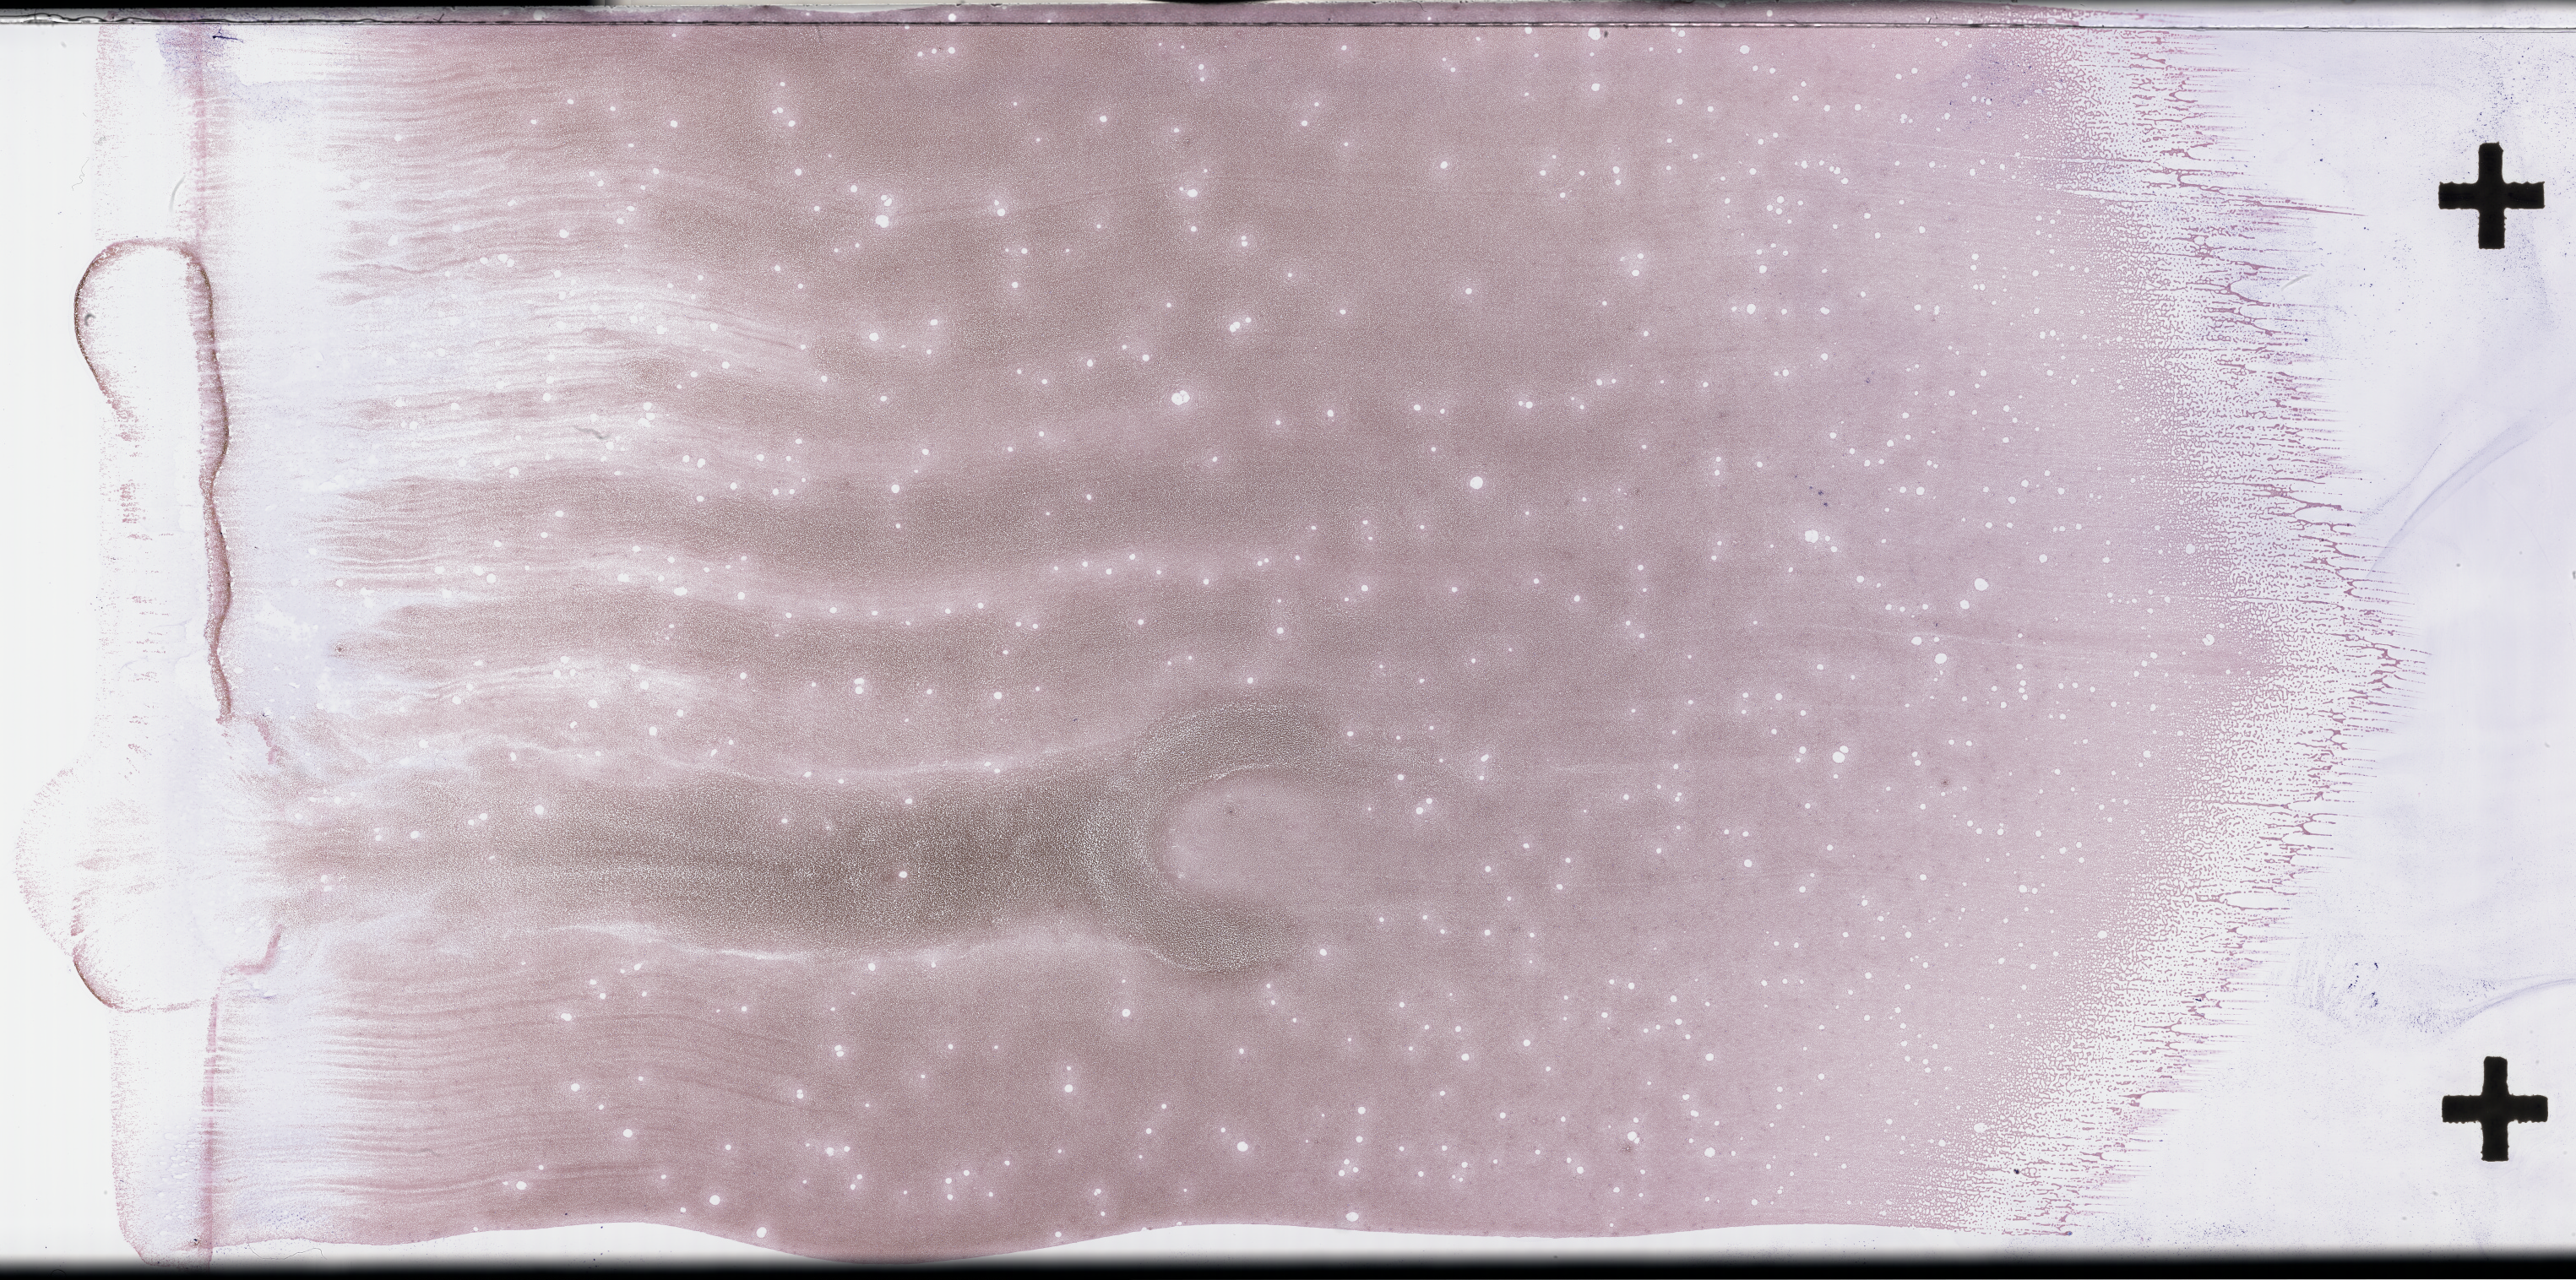
Wright–Giemsa-stained whole blood smear, whole-slide image — a low-resolution overview of the entire scanned area, about 49.3 x 24.5 mm. EDTA-anticoagulated smear. Male patient.
• patient diagnosis: Plasma Cell Myeloma